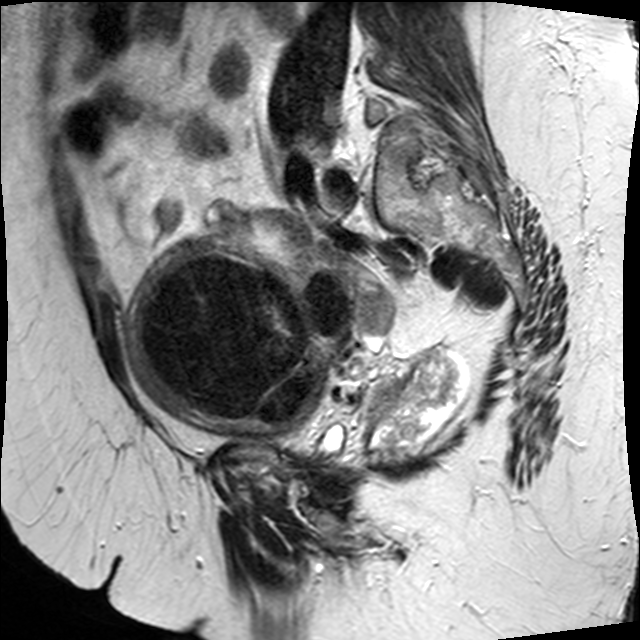
Pelvic MRI for cervical cancer, one sagittal slice. Slice 11 of 34 in the series (ordered by position). T2-weighted. 1.5 T. TE 89 ms, TR 3320 ms. 4 mm slice thickness. 640 × 640 image matrix, field of view 260 × 260 mm. Patient: female, 50 years.
Annotated regions visible in this slice (expert manual segmentation):
- uterus and cervix: bounding box [x1, y1, x2, y2] px = [129, 215, 462, 449]